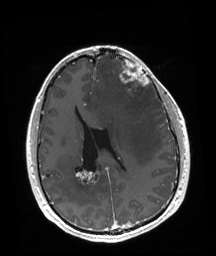
Brain MRI from a brain-tumour surgery series, one axial slice. Slice 74 of 192 in the series (ordered by position). T1-weighted post-contrast. 1 mm slice thickness. 216 × 256 image matrix, field of view 219 × 260 mm. Case-level facts recorded for this patient, not image findings: tumour location: Left Frontal.
Annotated regions visible in this slice (expert manual segmentation):
- tumour: box from (x=119, y=60) to (x=149, y=95) px